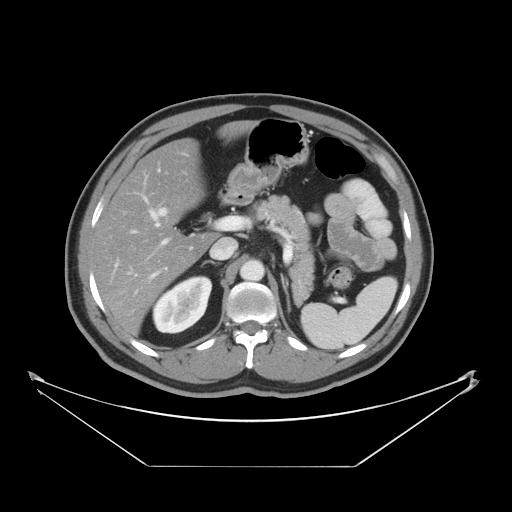
Contrast-enhanced abdominal CT, one axial slice. Reconstruction kernel STANDARD. Intravenous contrast given. Soft-tissue window (W 400 / L 40 HU). 5 mm slice thickness. 512 × 512 image matrix, field of view 465 × 465 mm. Male patient, age 57 years. From the clinical record (not read from this slice): diagnosis: colorectal cancer liver metastases, imaged before liver resection; multiple liver metastases: no; largest metastasis: 3.3 cm.
Annotated regions visible in this slice (expert manual segmentation):
- hepatic veins: bounding box (x1, y1, x2, y2) in pixels: (160, 207, 168, 217)
- liver: (96, 141, 217, 333)
- planned liver remnant (the part of the liver to remain after resection): (96, 141, 216, 333)
- portal vein (with intrahepatic branches): (130, 198, 267, 283)